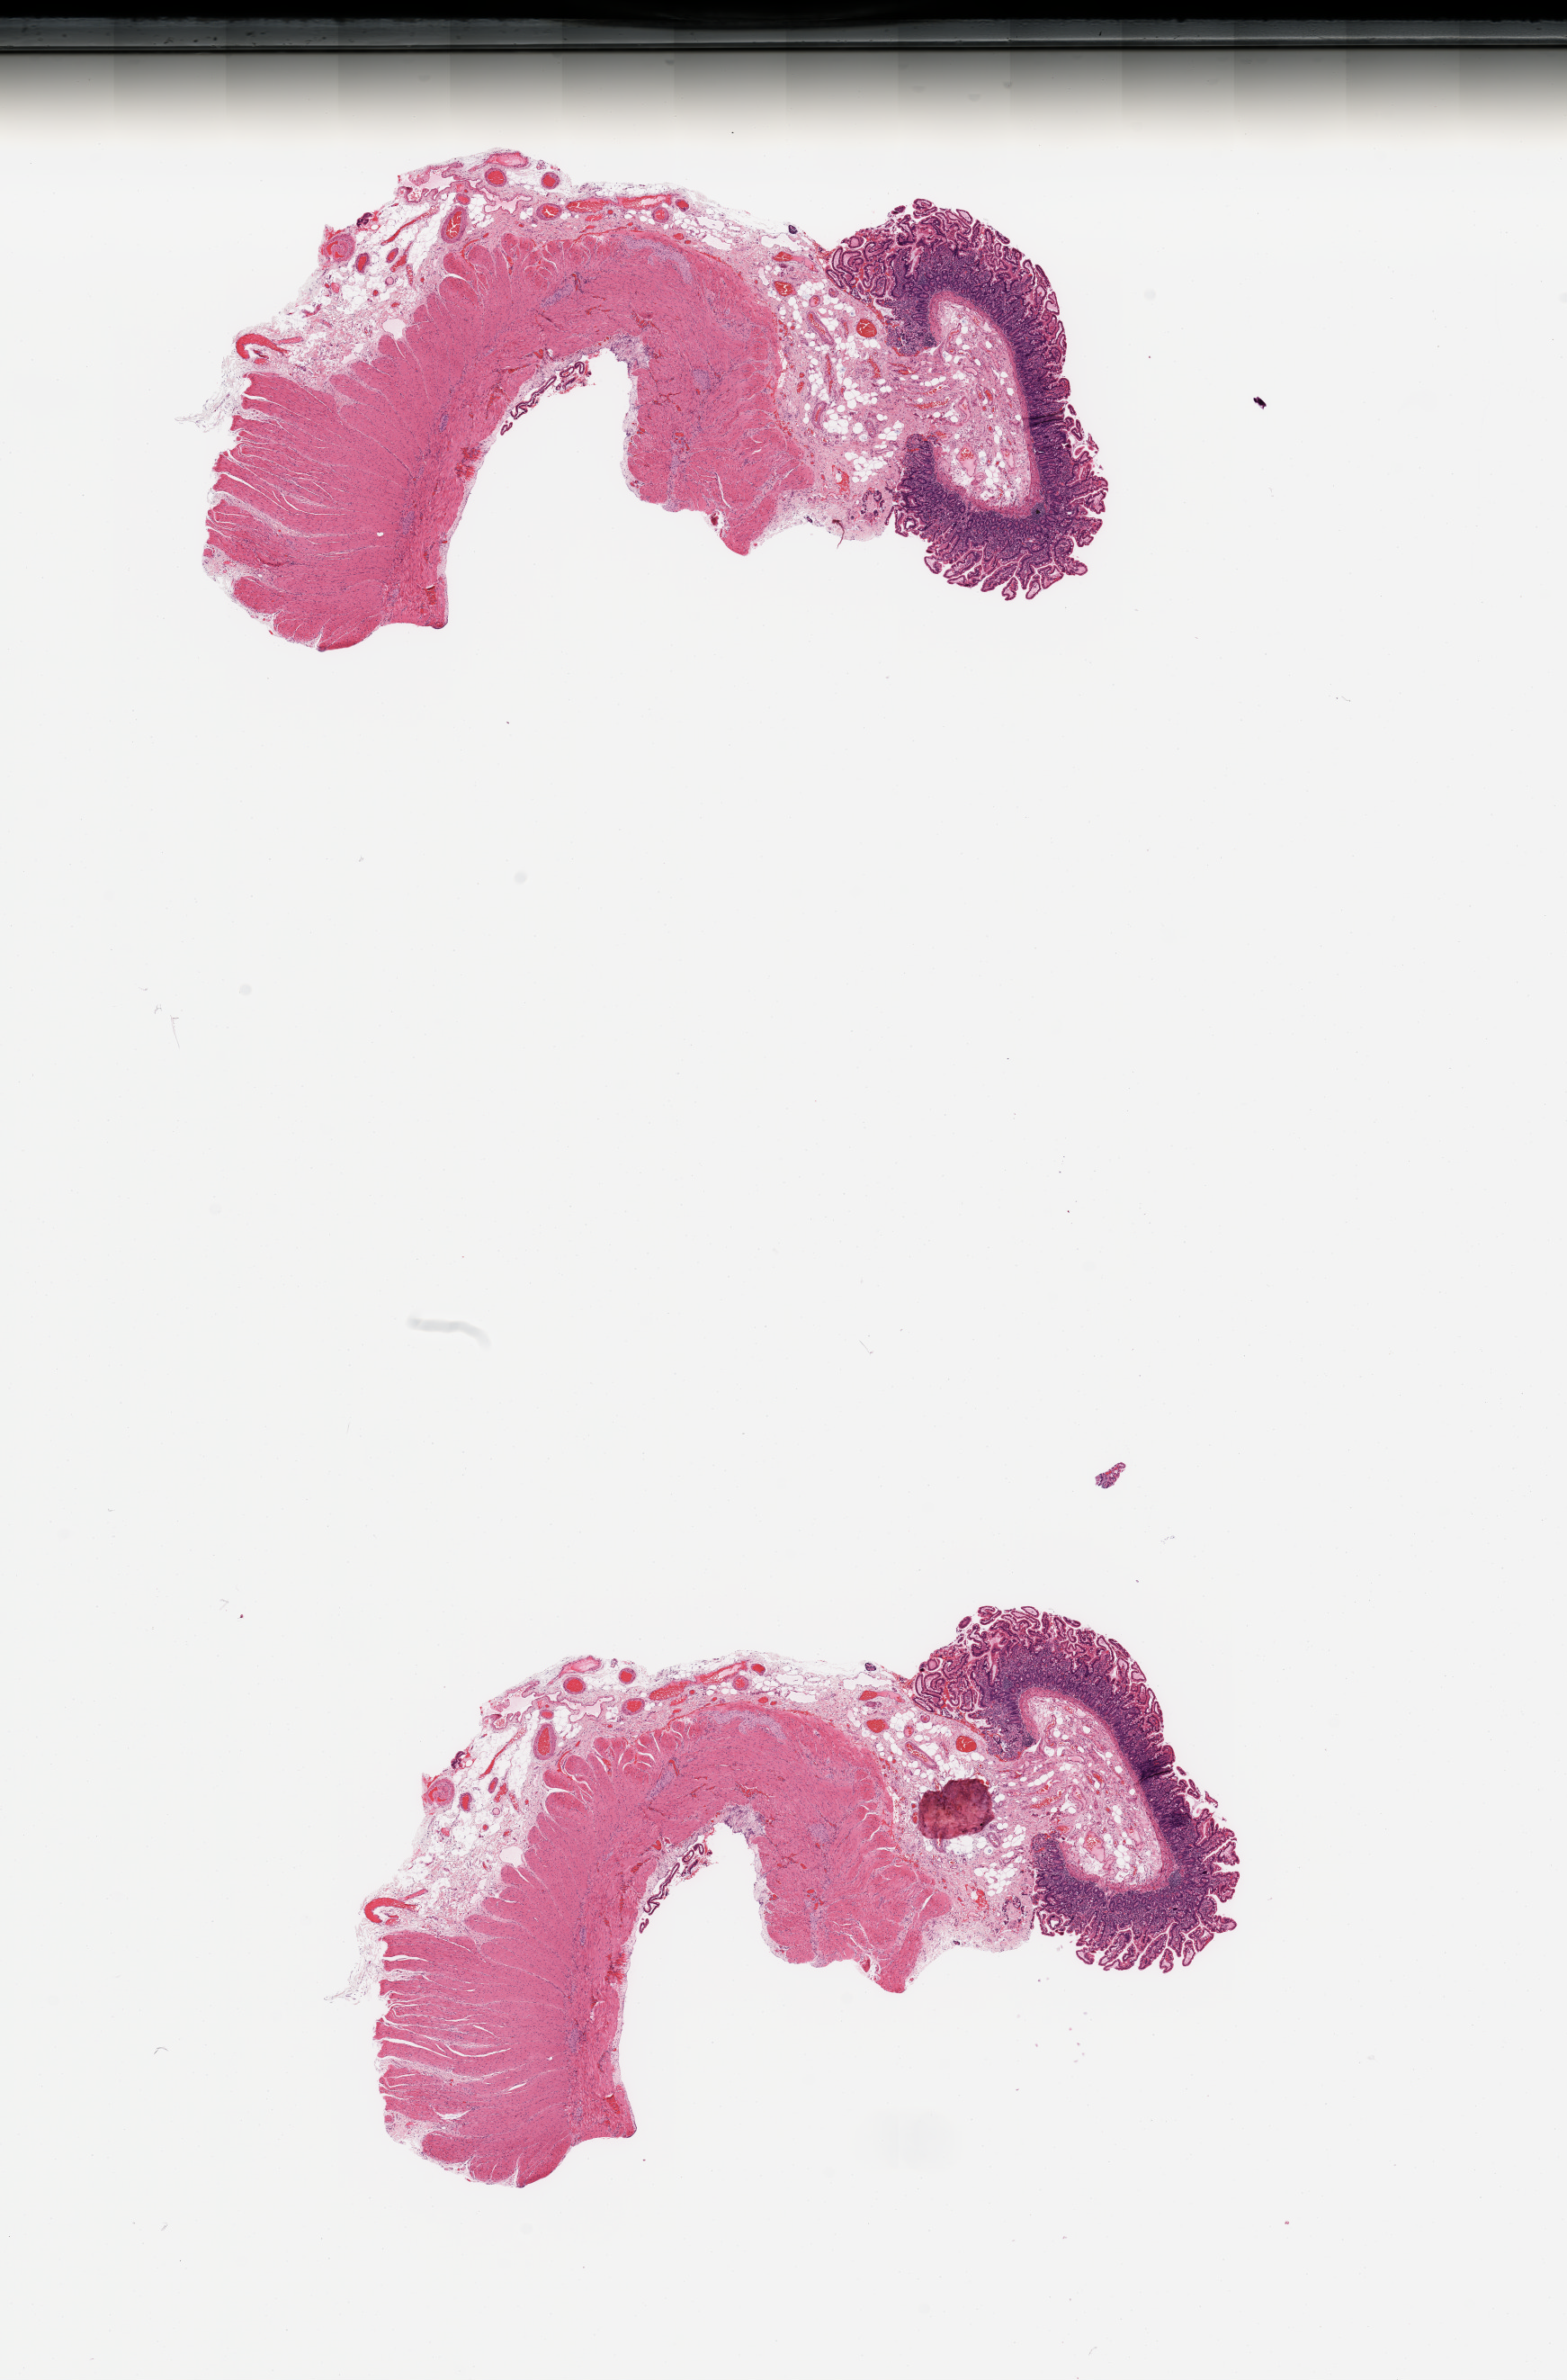
H&E-stained whole-slide image — a low-resolution overview of the entire scanned area, about 13.8 x 20.9 mm, normal (non-tumour) tissue sample, sampled site: pancreas. Patient: male, age 80 years.
This section: normal (non-tumour) tissue from the same patient. Patient diagnosis: Infiltrating duct carcinoma, NOS.